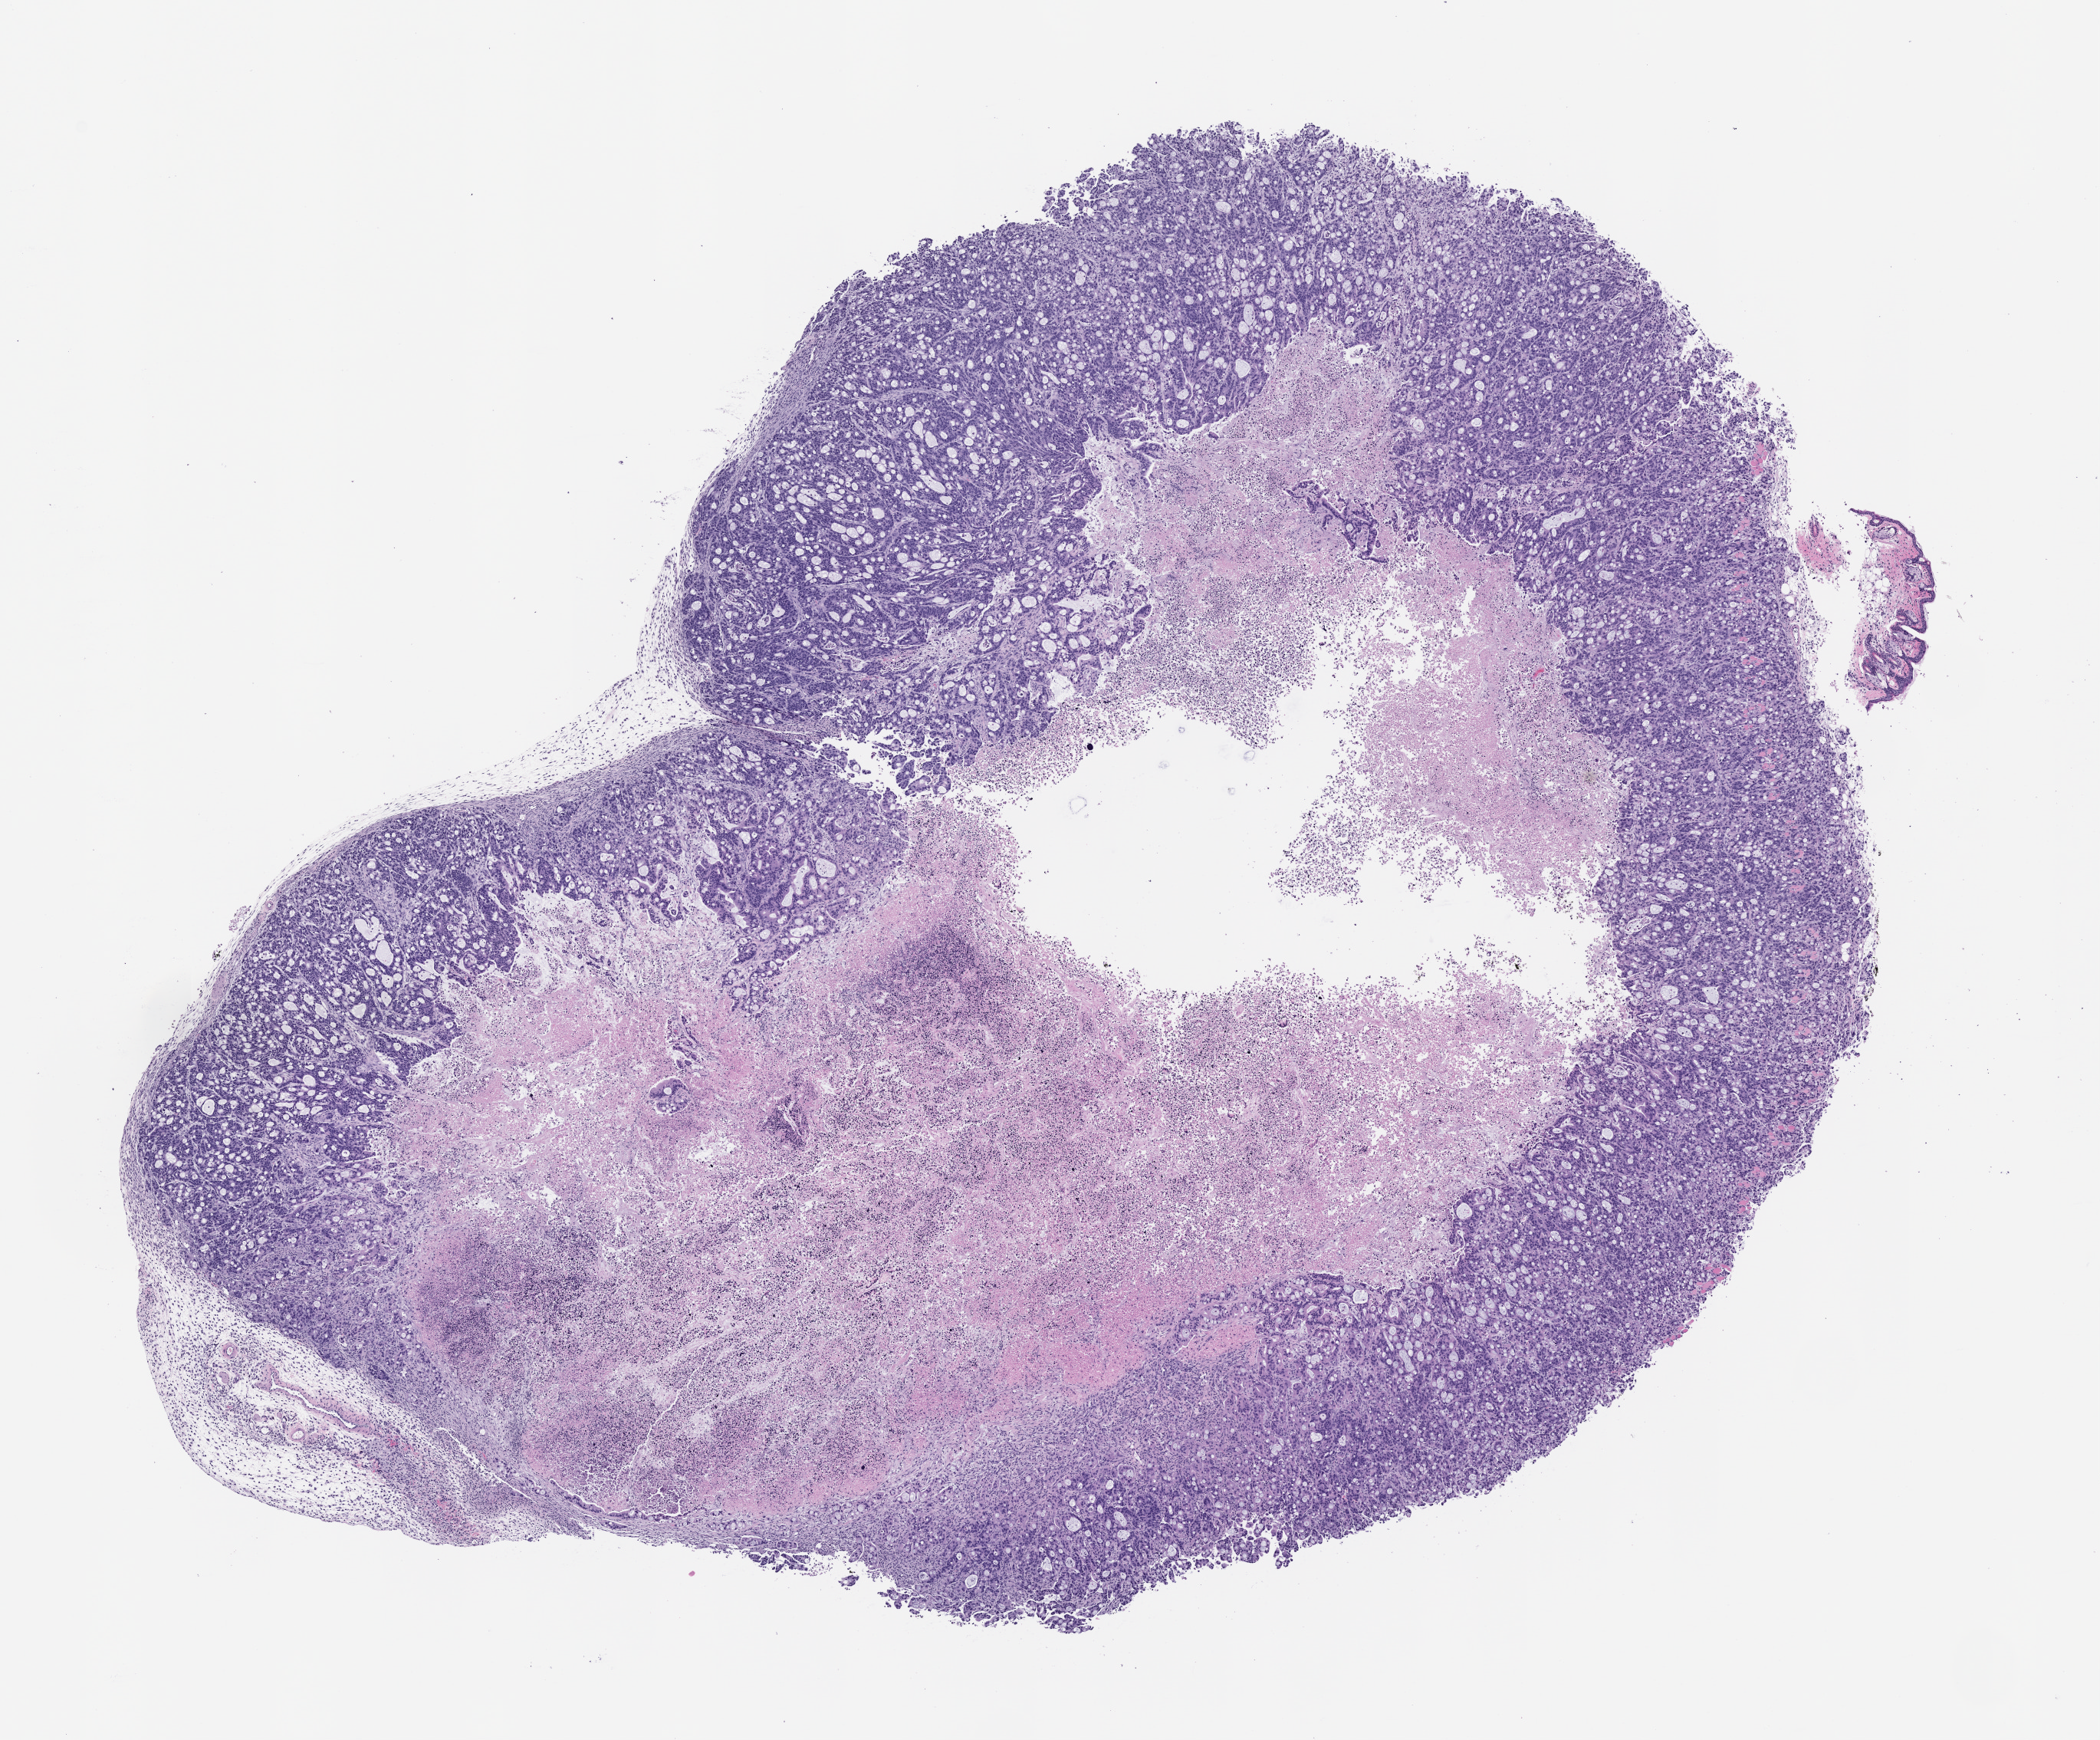
Haematoxylin and eosin whole-slide image of a patient-derived xenograft (PDX) tumor grown in a mouse, passage 1, whole scanned area (about 11.0 x 9.1 mm) shown as a low-resolution overview. Formalin-fixed, paraffin-embedded (FFPE) tissue. Originating tumor site category: colon.
Originating patient diagnosis: Colon Adenocarcinoma.